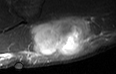
MRI of an extremity soft-tissue mass, one axial slice; slice 18 of 36 in the series (ordered by position); STIR; MR volume resampled by the dataset authors to the PET/CT grid (not the native acquisition matrix); 3.27 mm slice thickness; 116 × 74 image matrix, field of view 113 × 72 mm. Male patient. Case-level facts recorded for this patient, not image findings: histological type: pleiomorphic leiomyosarcoma; grade: high; site of the primary tumour: left buttock.
Structures marked on this image (expert contour drawn on MRI and transferred to this co-registered scan by the dataset authors):
- gross tumour volume including surrounding oedema: bounding box <28,17,86,56> (left, top, right, bottom; pixels)
- gross tumour volume (mass): <28,17,85,56>